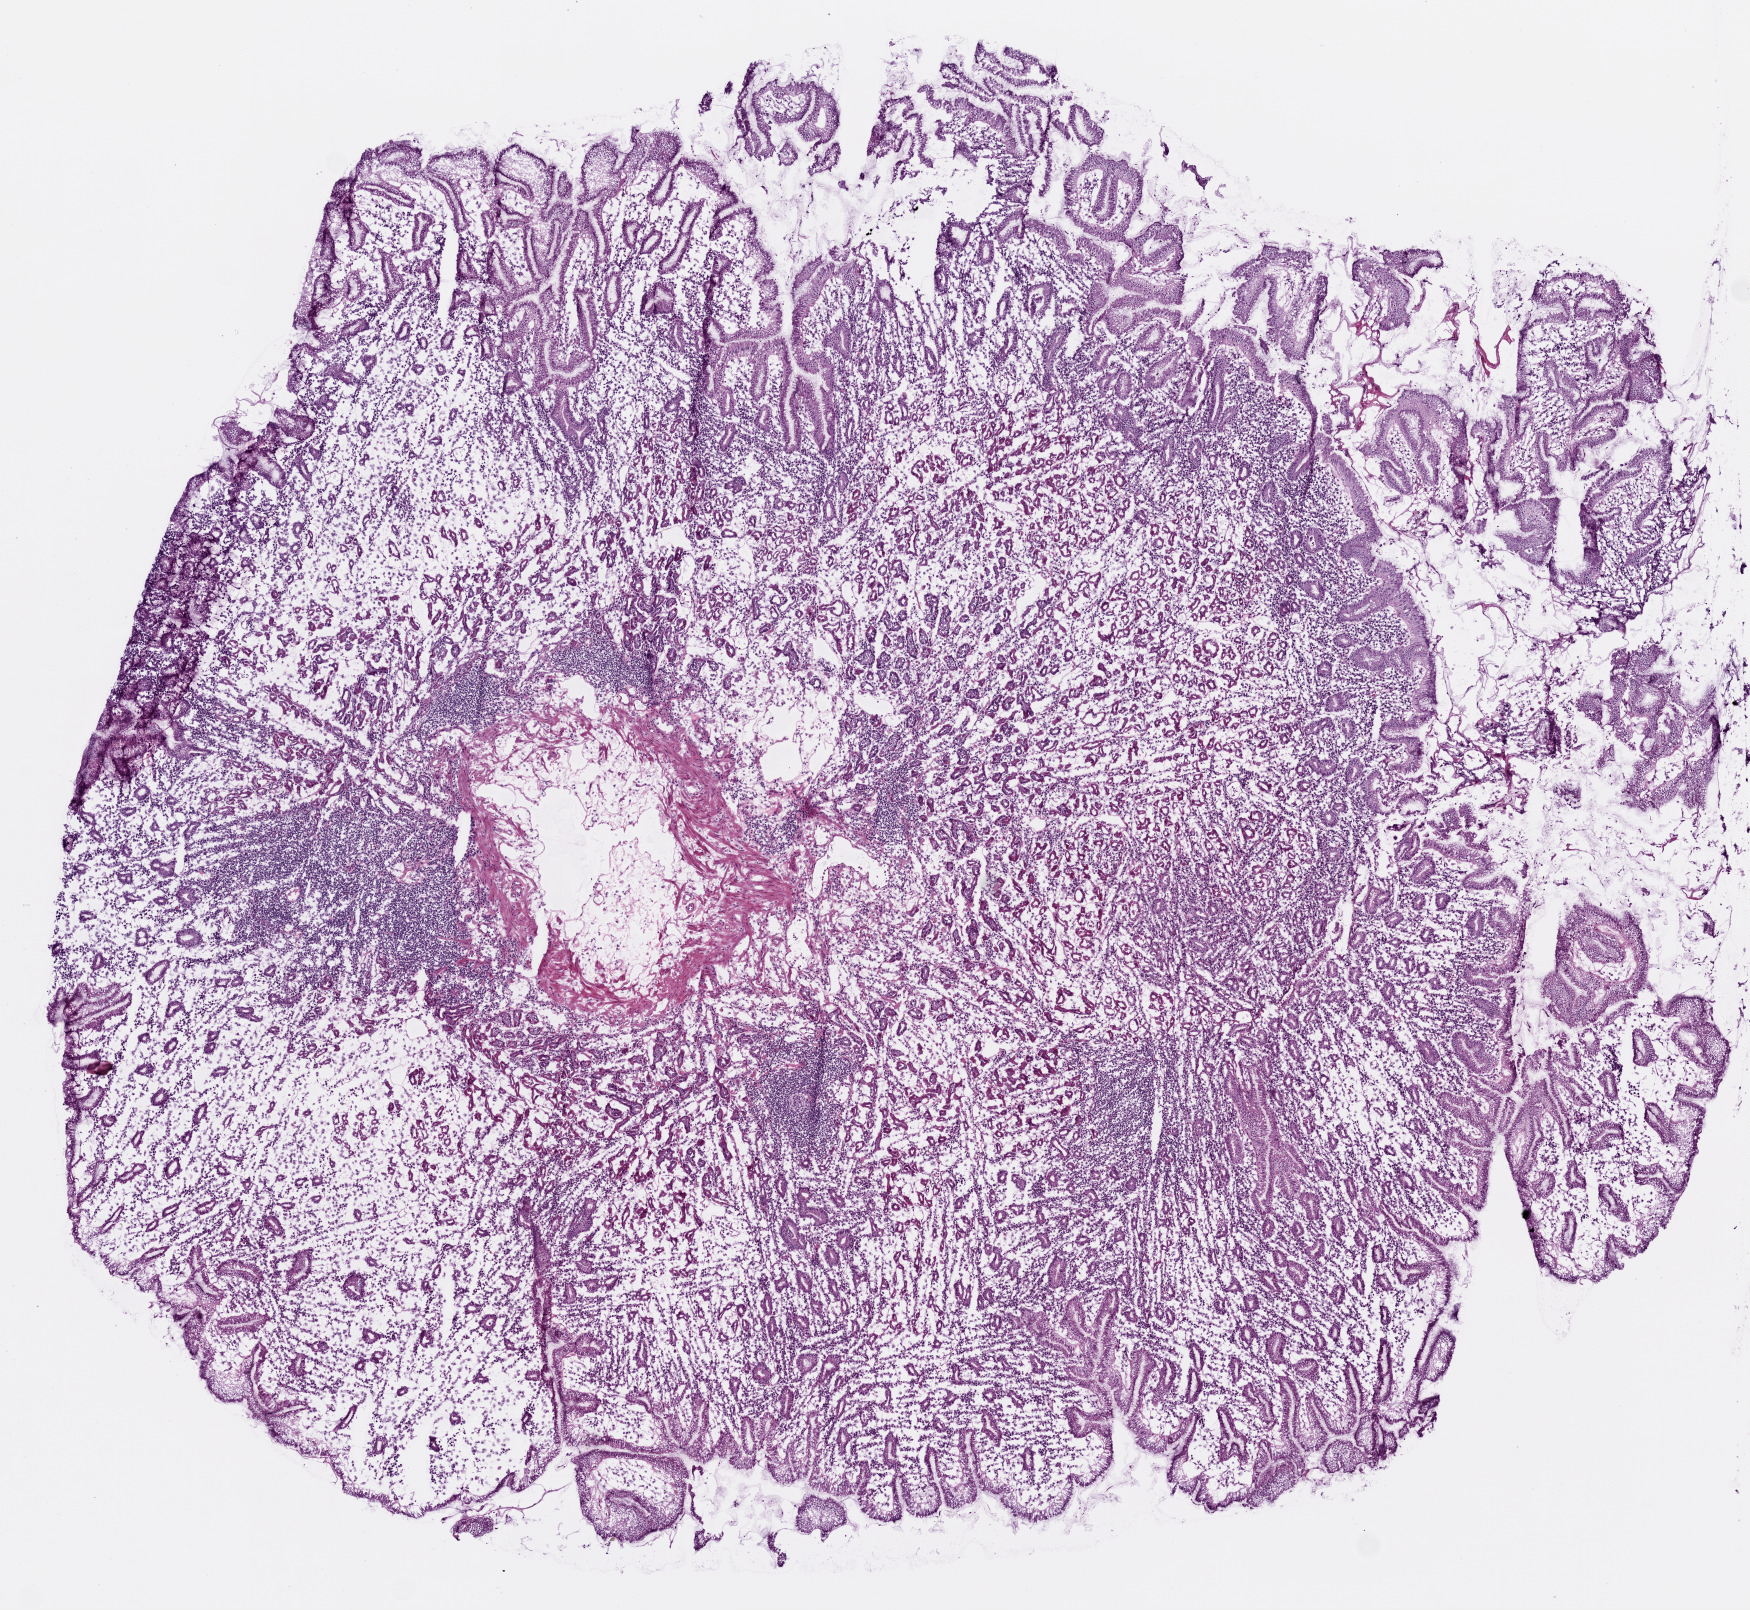
Digitized Hematoxylin and eosin (H&E) stained tissue section (whole slide) — low-resolution overview of the scanned area, about 7.0 x 6.5 mm (from a 20x scan). Frozen section from the top of the tissue portion. Sample: solid tissue normal (non-tumour tissue), stomach. Patient sex: female.
This section: solid tissue normal (non-tumour) sample from the same patient. Patient diagnosis: Adenocarcinoma, intestinal type (gastric antrum).